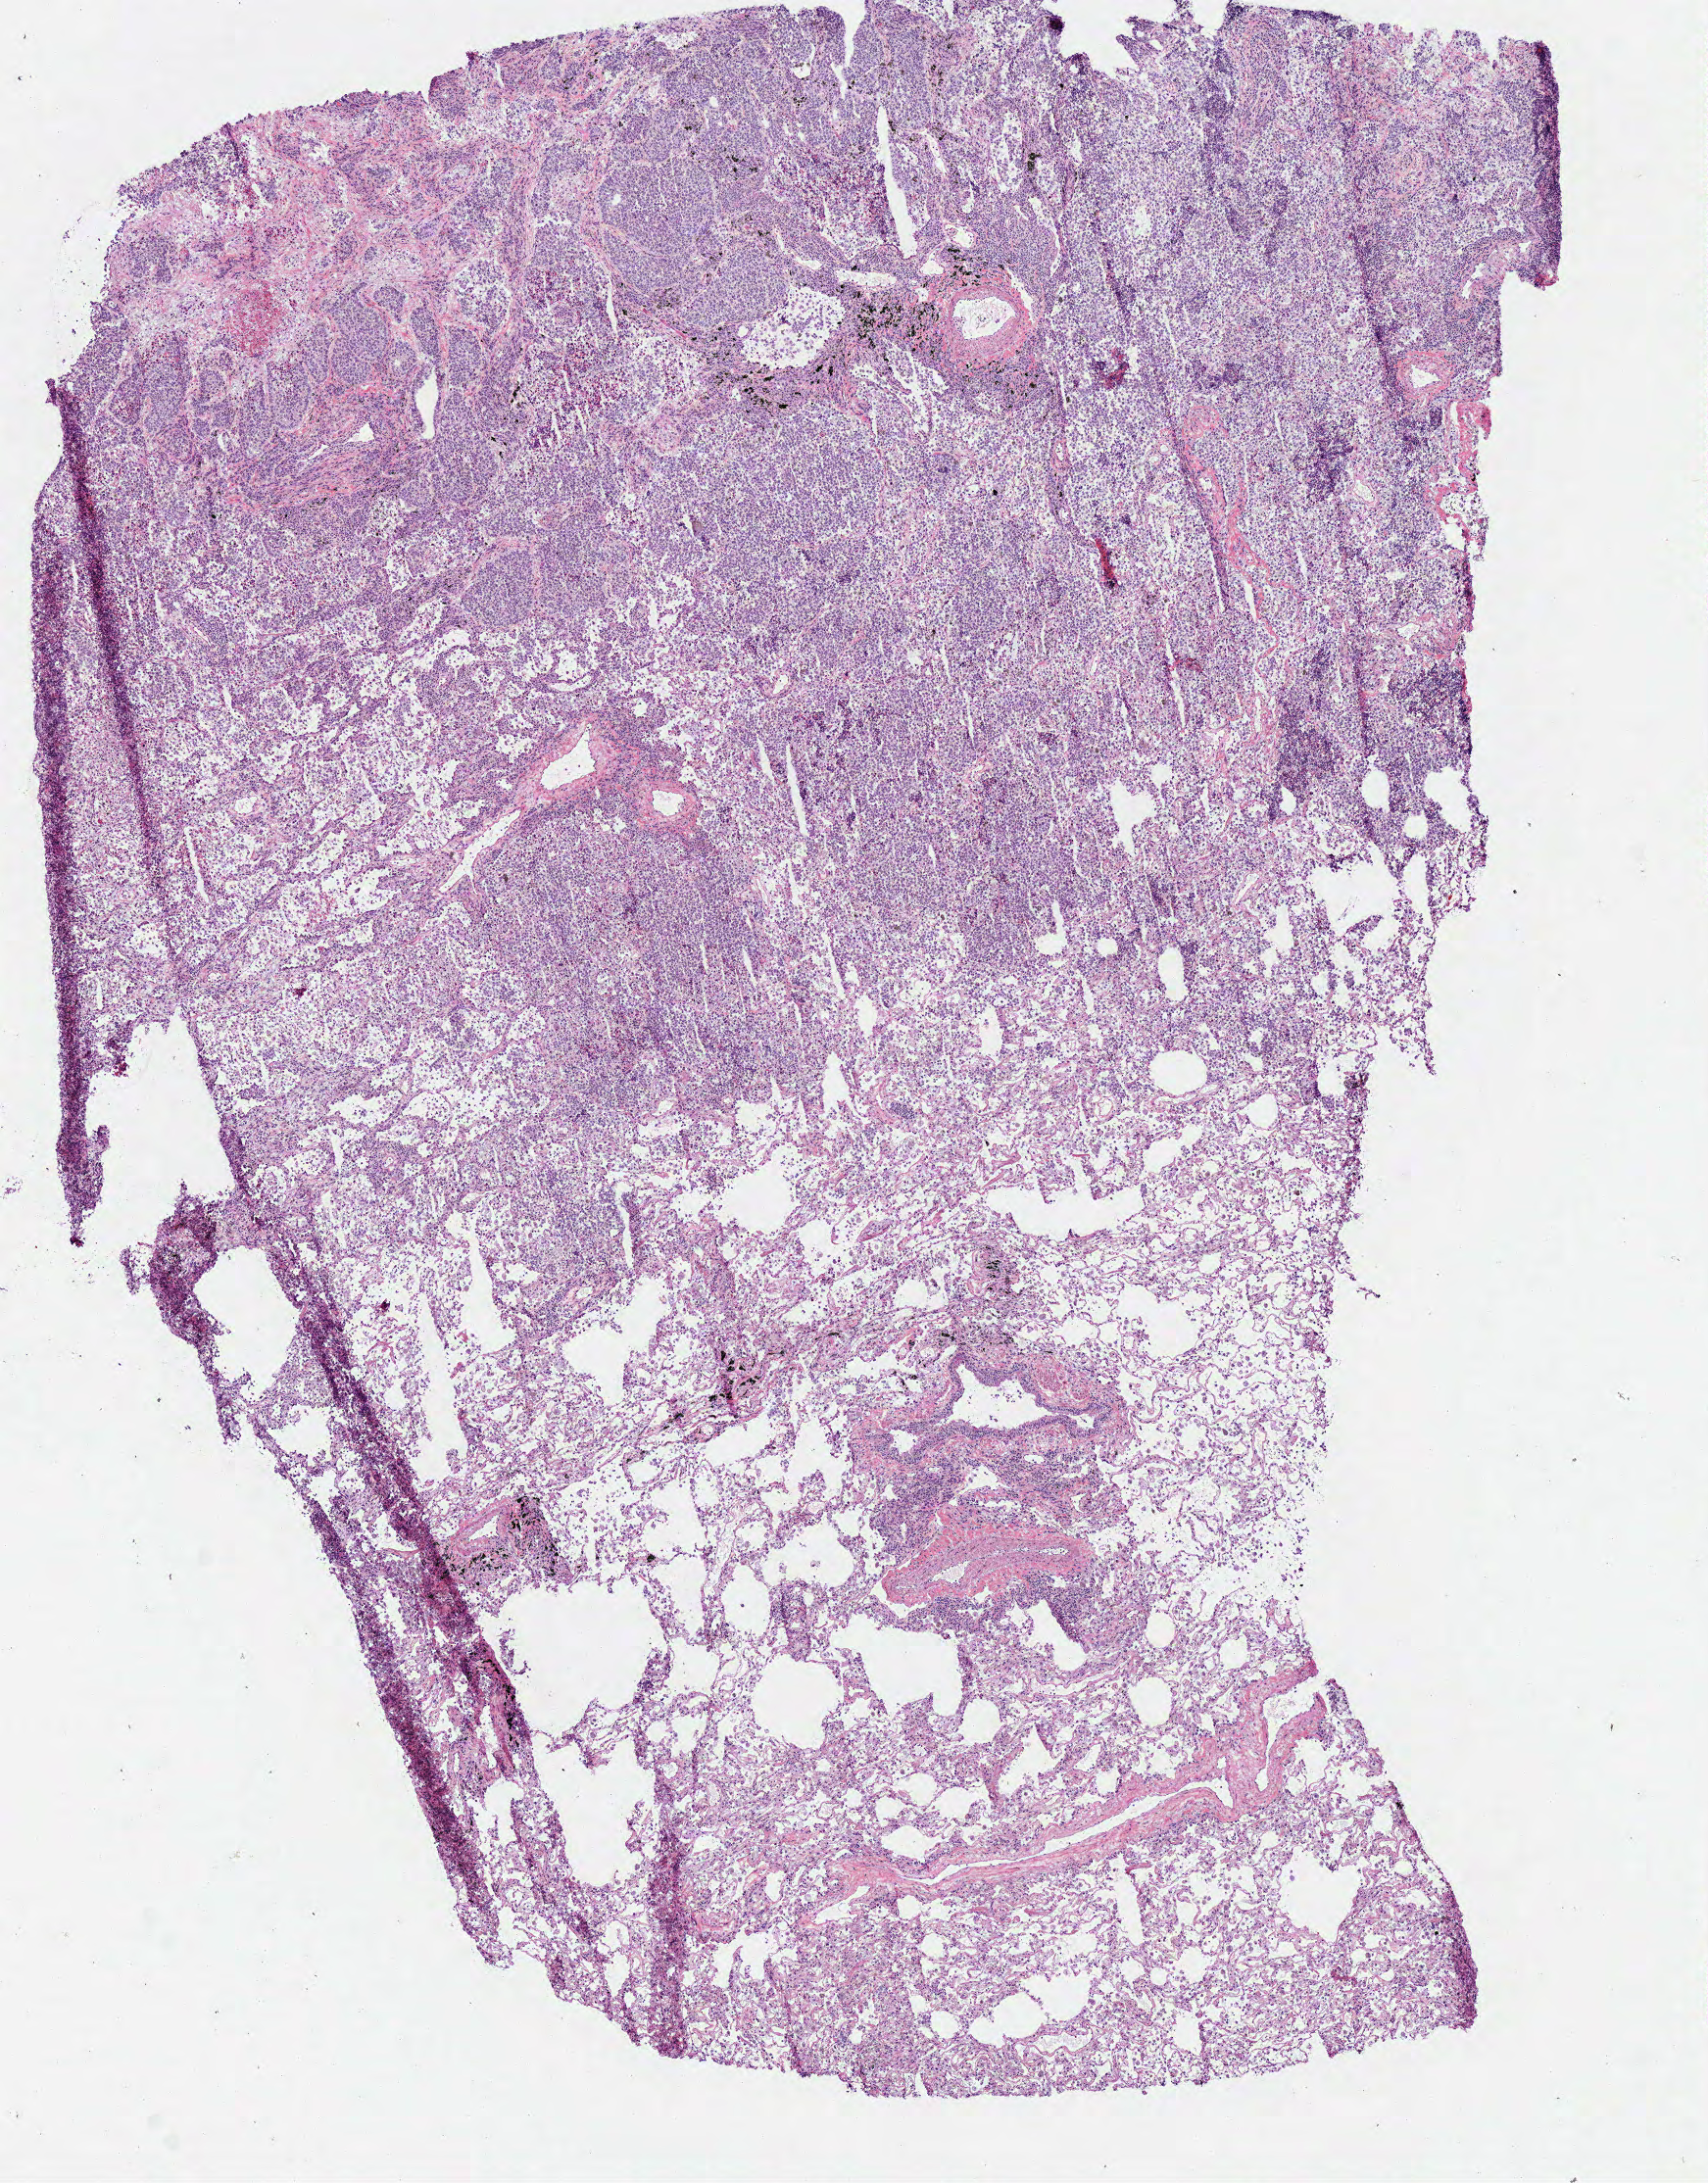
Digitized H&E tissue section (whole slide), whole scanned area (about 6.9 x 8.8 mm) shown as a low-resolution overview, frozen section from the bottom of the tissue portion, primary tumour sample from the lung. Male patient; age at initial diagnosis 59 years. Composition of this section per pathologist review: tumour cells 55%, tumour nuclei 50%, normal cells 40%, stromal cells 0%, necrosis 5%. Infiltration values recorded for this section: lymphocyte infiltration 25%, monocyte infiltration 5%, neutrophil infiltration 10%.
AJCC pathologic stage: IA (6th edition). Pathologic diagnosis: Adenocarcinoma, NOS.